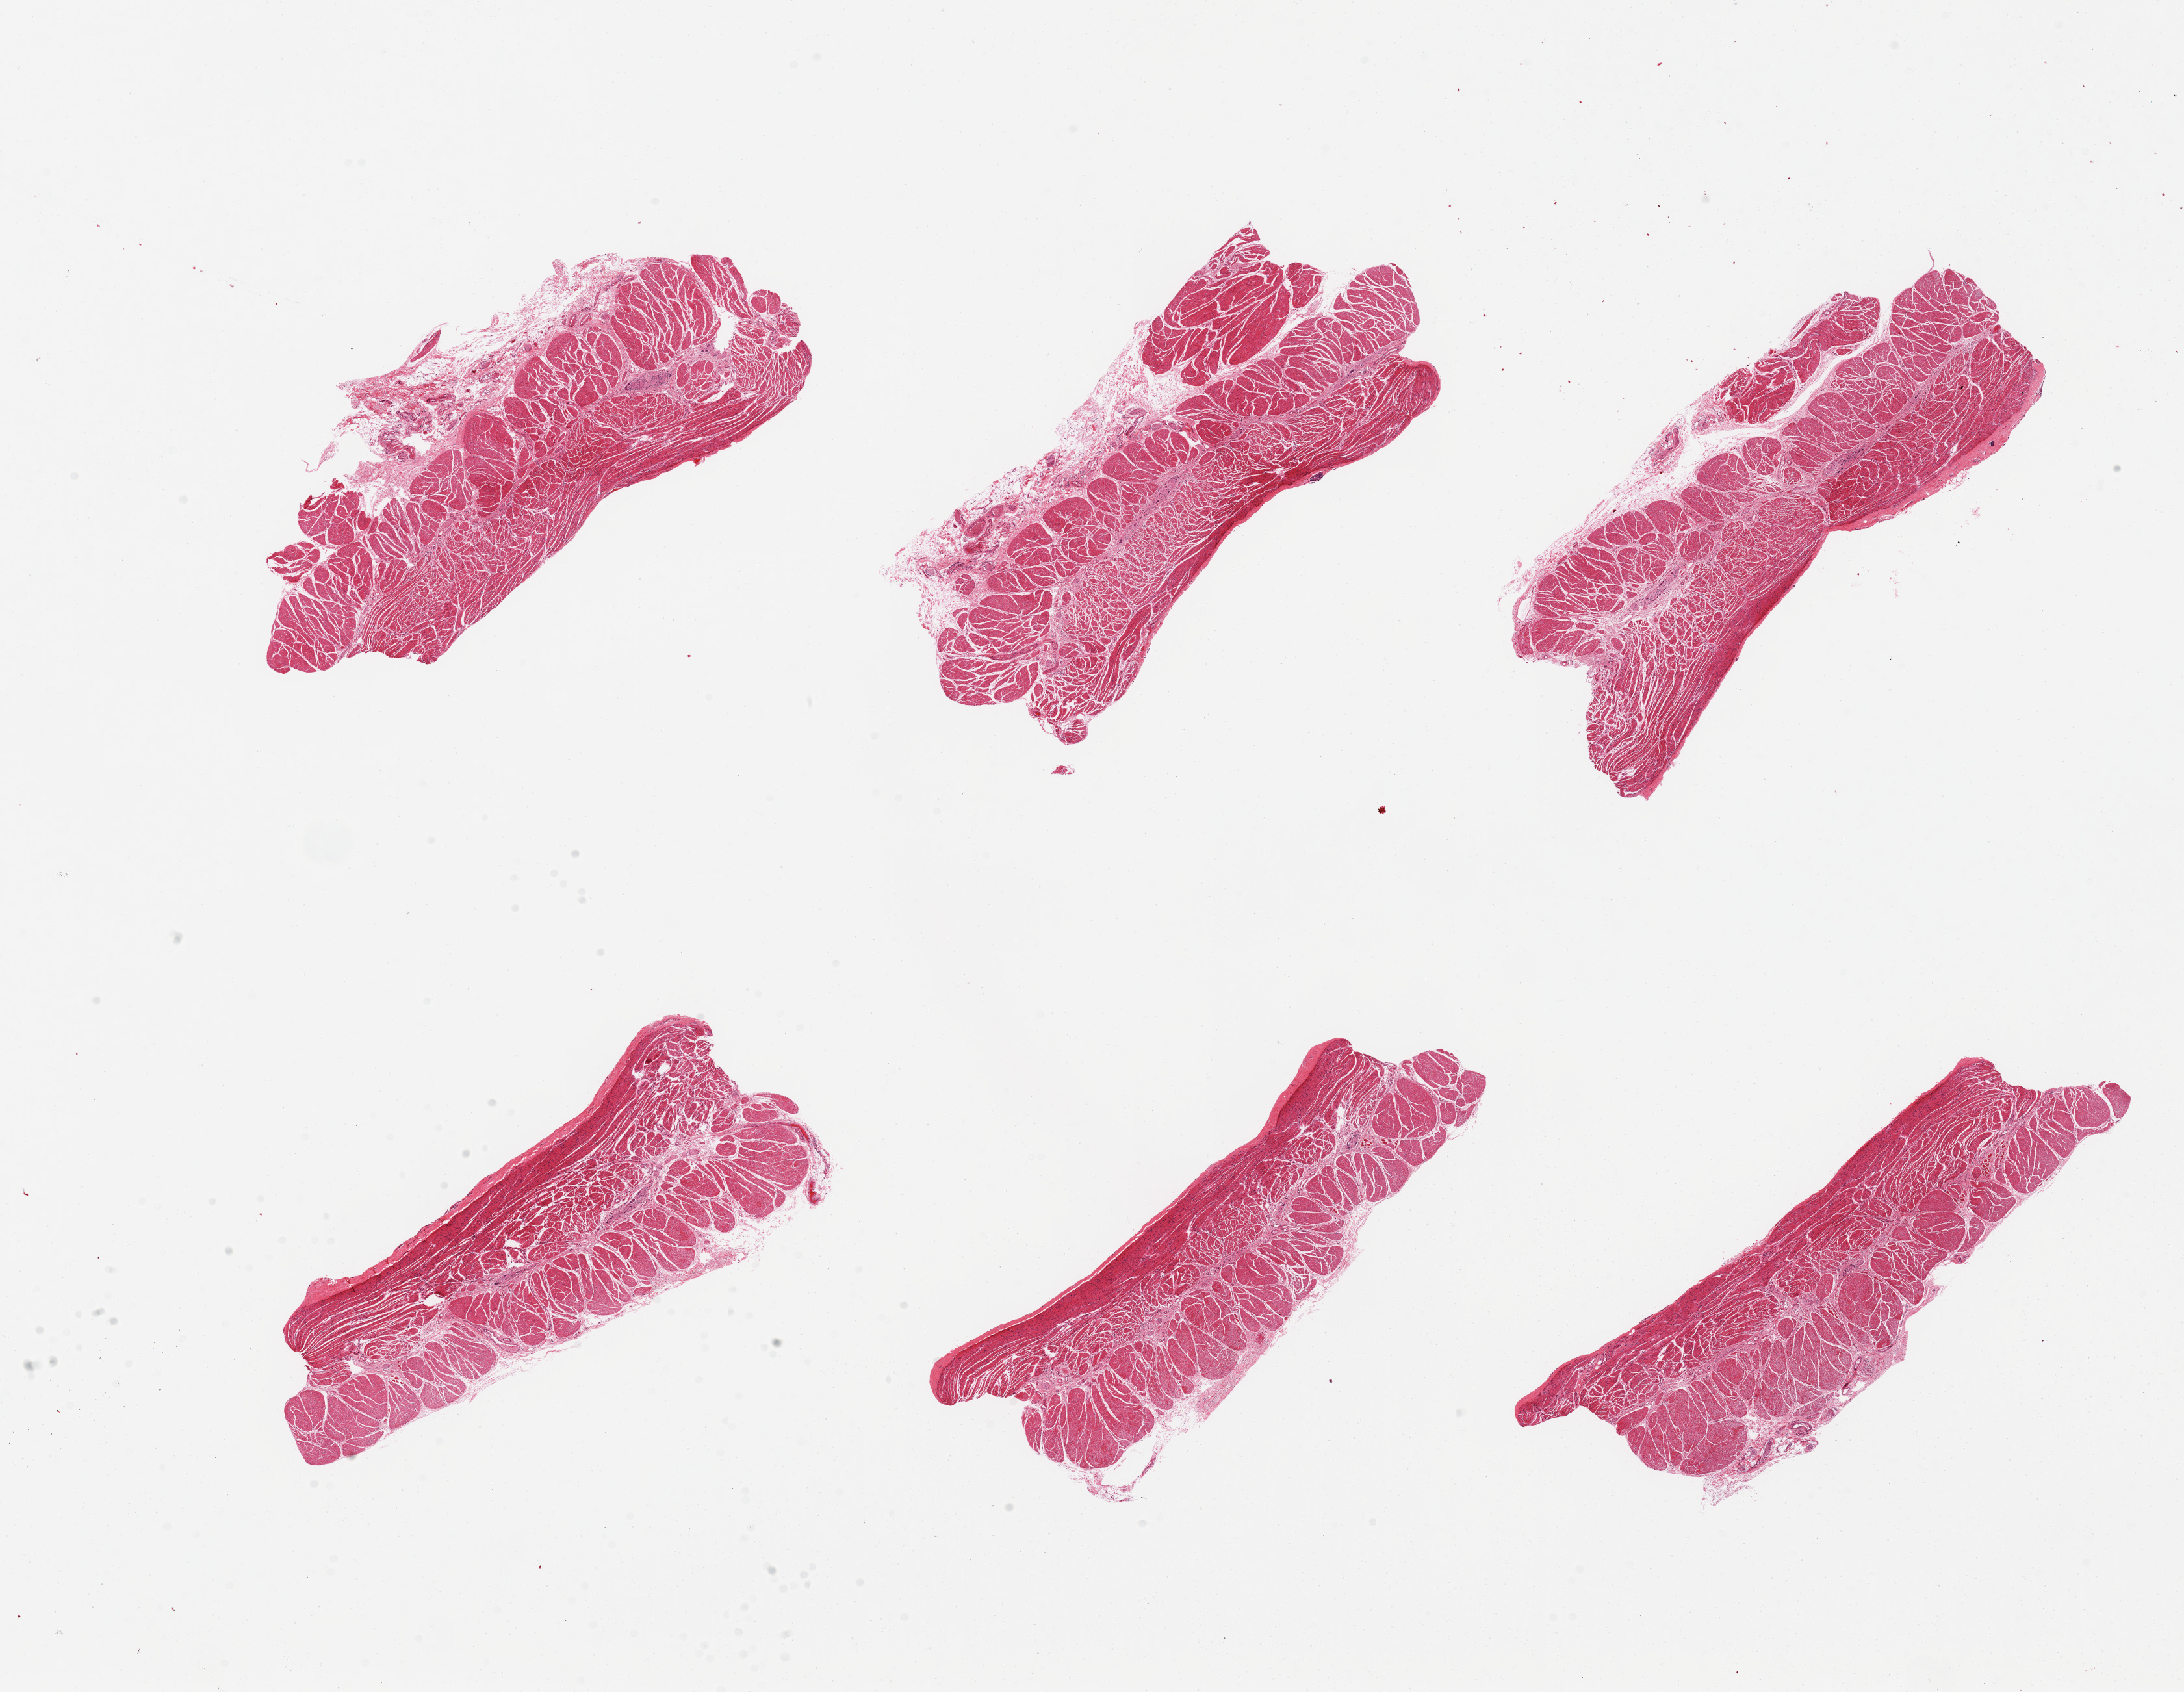
H&E whole-slide image, brightfield — whole scanned area (about 26.6 x 20.6 mm, slide scanned at 20x) shown as a low-resolution overview. PAXgene-fixed paraffin-embedded (PFPE) section. Sampled site (target tissue): esophageal muscle. Donor tissue sample. Donor sex: male.
- pathologist's review note for this sample: 6 pieces, all muscularis